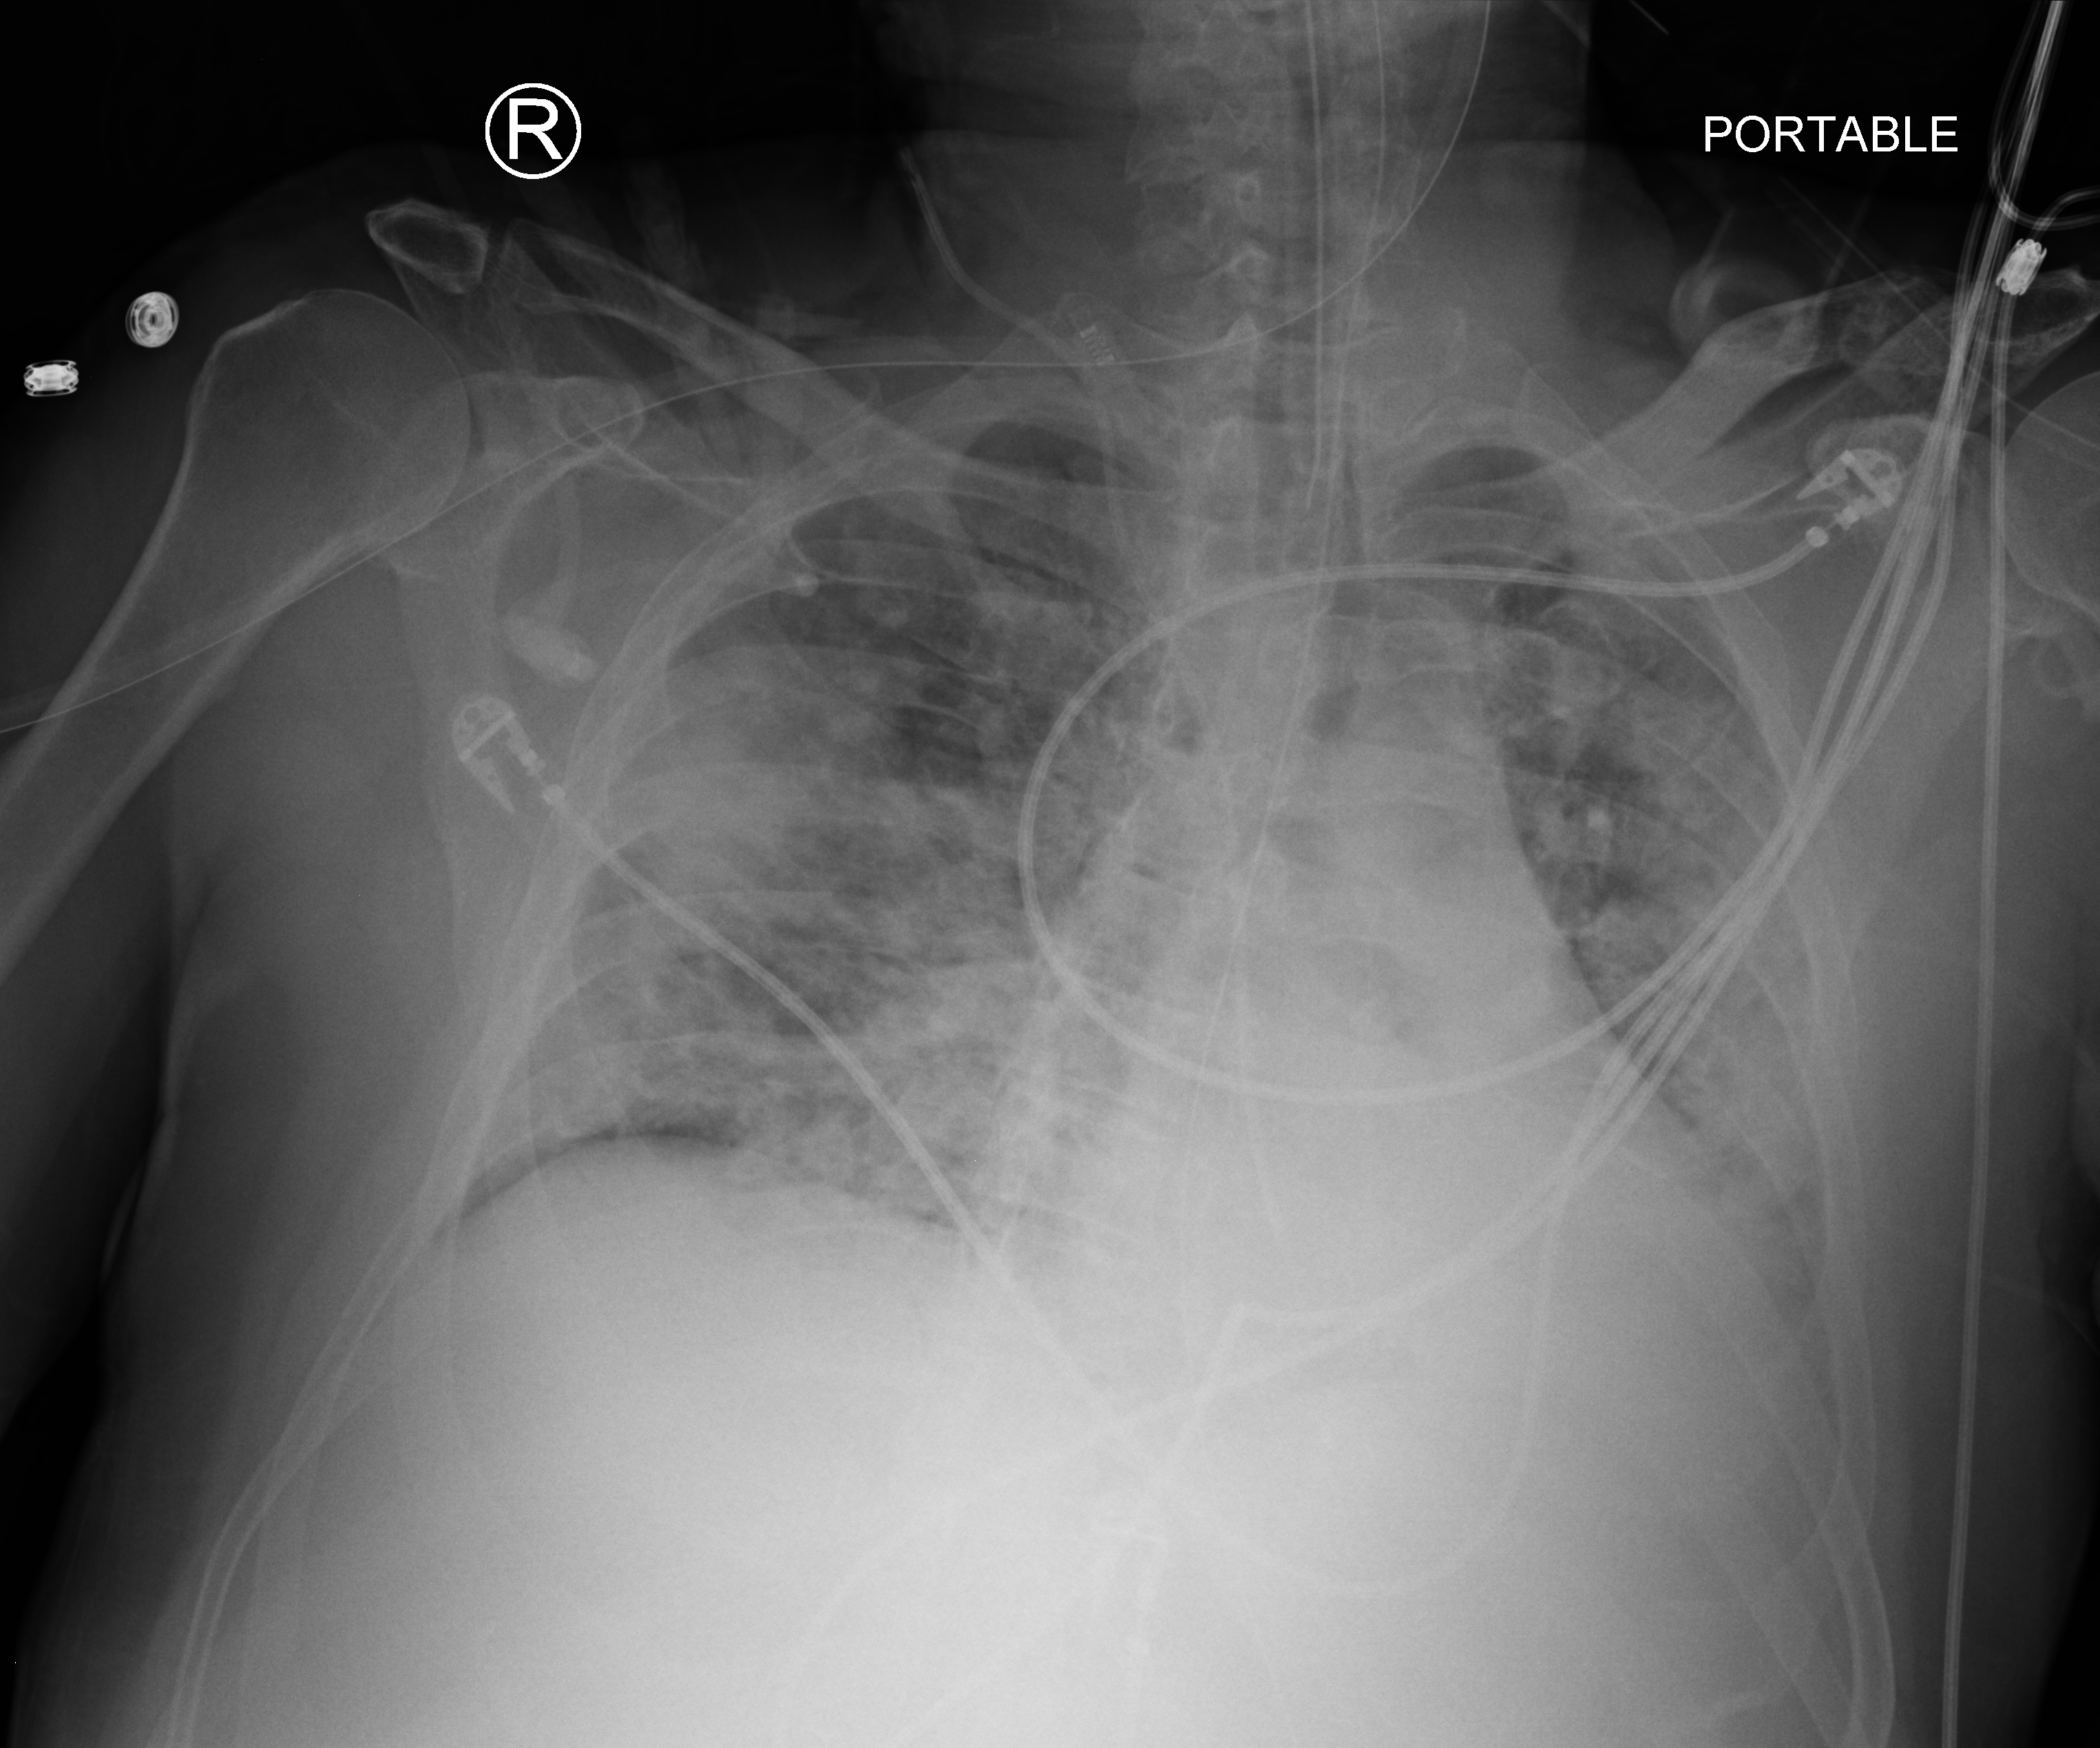
Portable chest radiograph; anteroposterior (AP) projection. Patient hospitalised with COVID-19; male, aged 18–59 years.
Admission-level facts for this patient (not findings on this image; timing relative to this image not recorded): admitted to intensive care during this hospital stay: yes; COPD (admission record): no; diabetes (admission record): no.